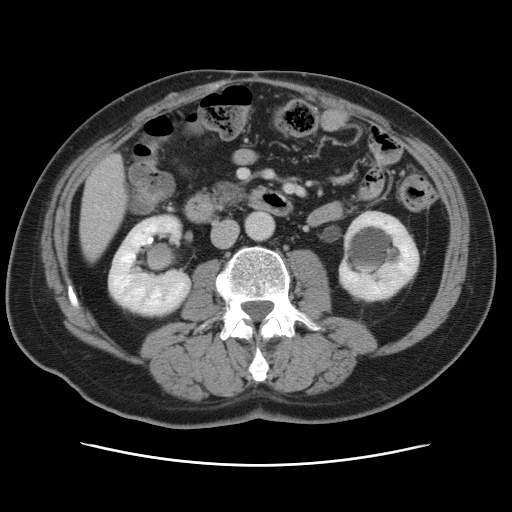
Contrast-enhanced abdominal CT, one axial slice; position 19 of 80 along the scan axis; intravenous contrast given; soft-tissue window (W 400 / L 40 HU); 5 mm slice thickness; 512 × 512 image matrix, field of view 370 × 370 mm. Male patient, age 69 years. From the clinical record (not read from this slice): diagnosis: colorectal cancer liver metastases, imaged before liver resection; multiple liver metastases: no; largest metastasis: 5 cm; disease in both lobes: yes.
Structures marked on this image (manually delineated by an expert):
- liver: bounding box <80,156,127,258> (left, top, right, bottom; pixels)
- planned liver remnant (the part of the liver to remain after resection): <80,225,115,257>